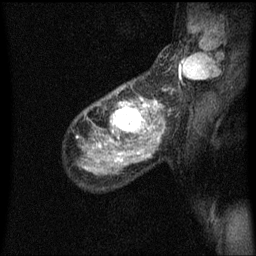
Breast MRI (dynamic contrast-enhanced), one sagittal slice. Position 42 of 60 along the scan axis. Dynamic contrast-enhanced series, image 2 of 3 at this slice position (ordered by acquisition). 1.5 T. TE 4.2 ms, TR 8.4 ms. 2 mm slice thickness. 256 × 256 image matrix. Female patient, age 49 years.
Annotated regions visible in this slice (semi-automatically segmented with operator editing):
- analysis volume of interest (the breast-tissue region the enhancement analysis was run in; not a lesion): box from (x=103, y=90) to (x=157, y=151) px
- tumour enhancement mask (voxels above the 70 % enhancement threshold inside the analysis volume of interest): (x=111, y=100)–(x=157, y=133)